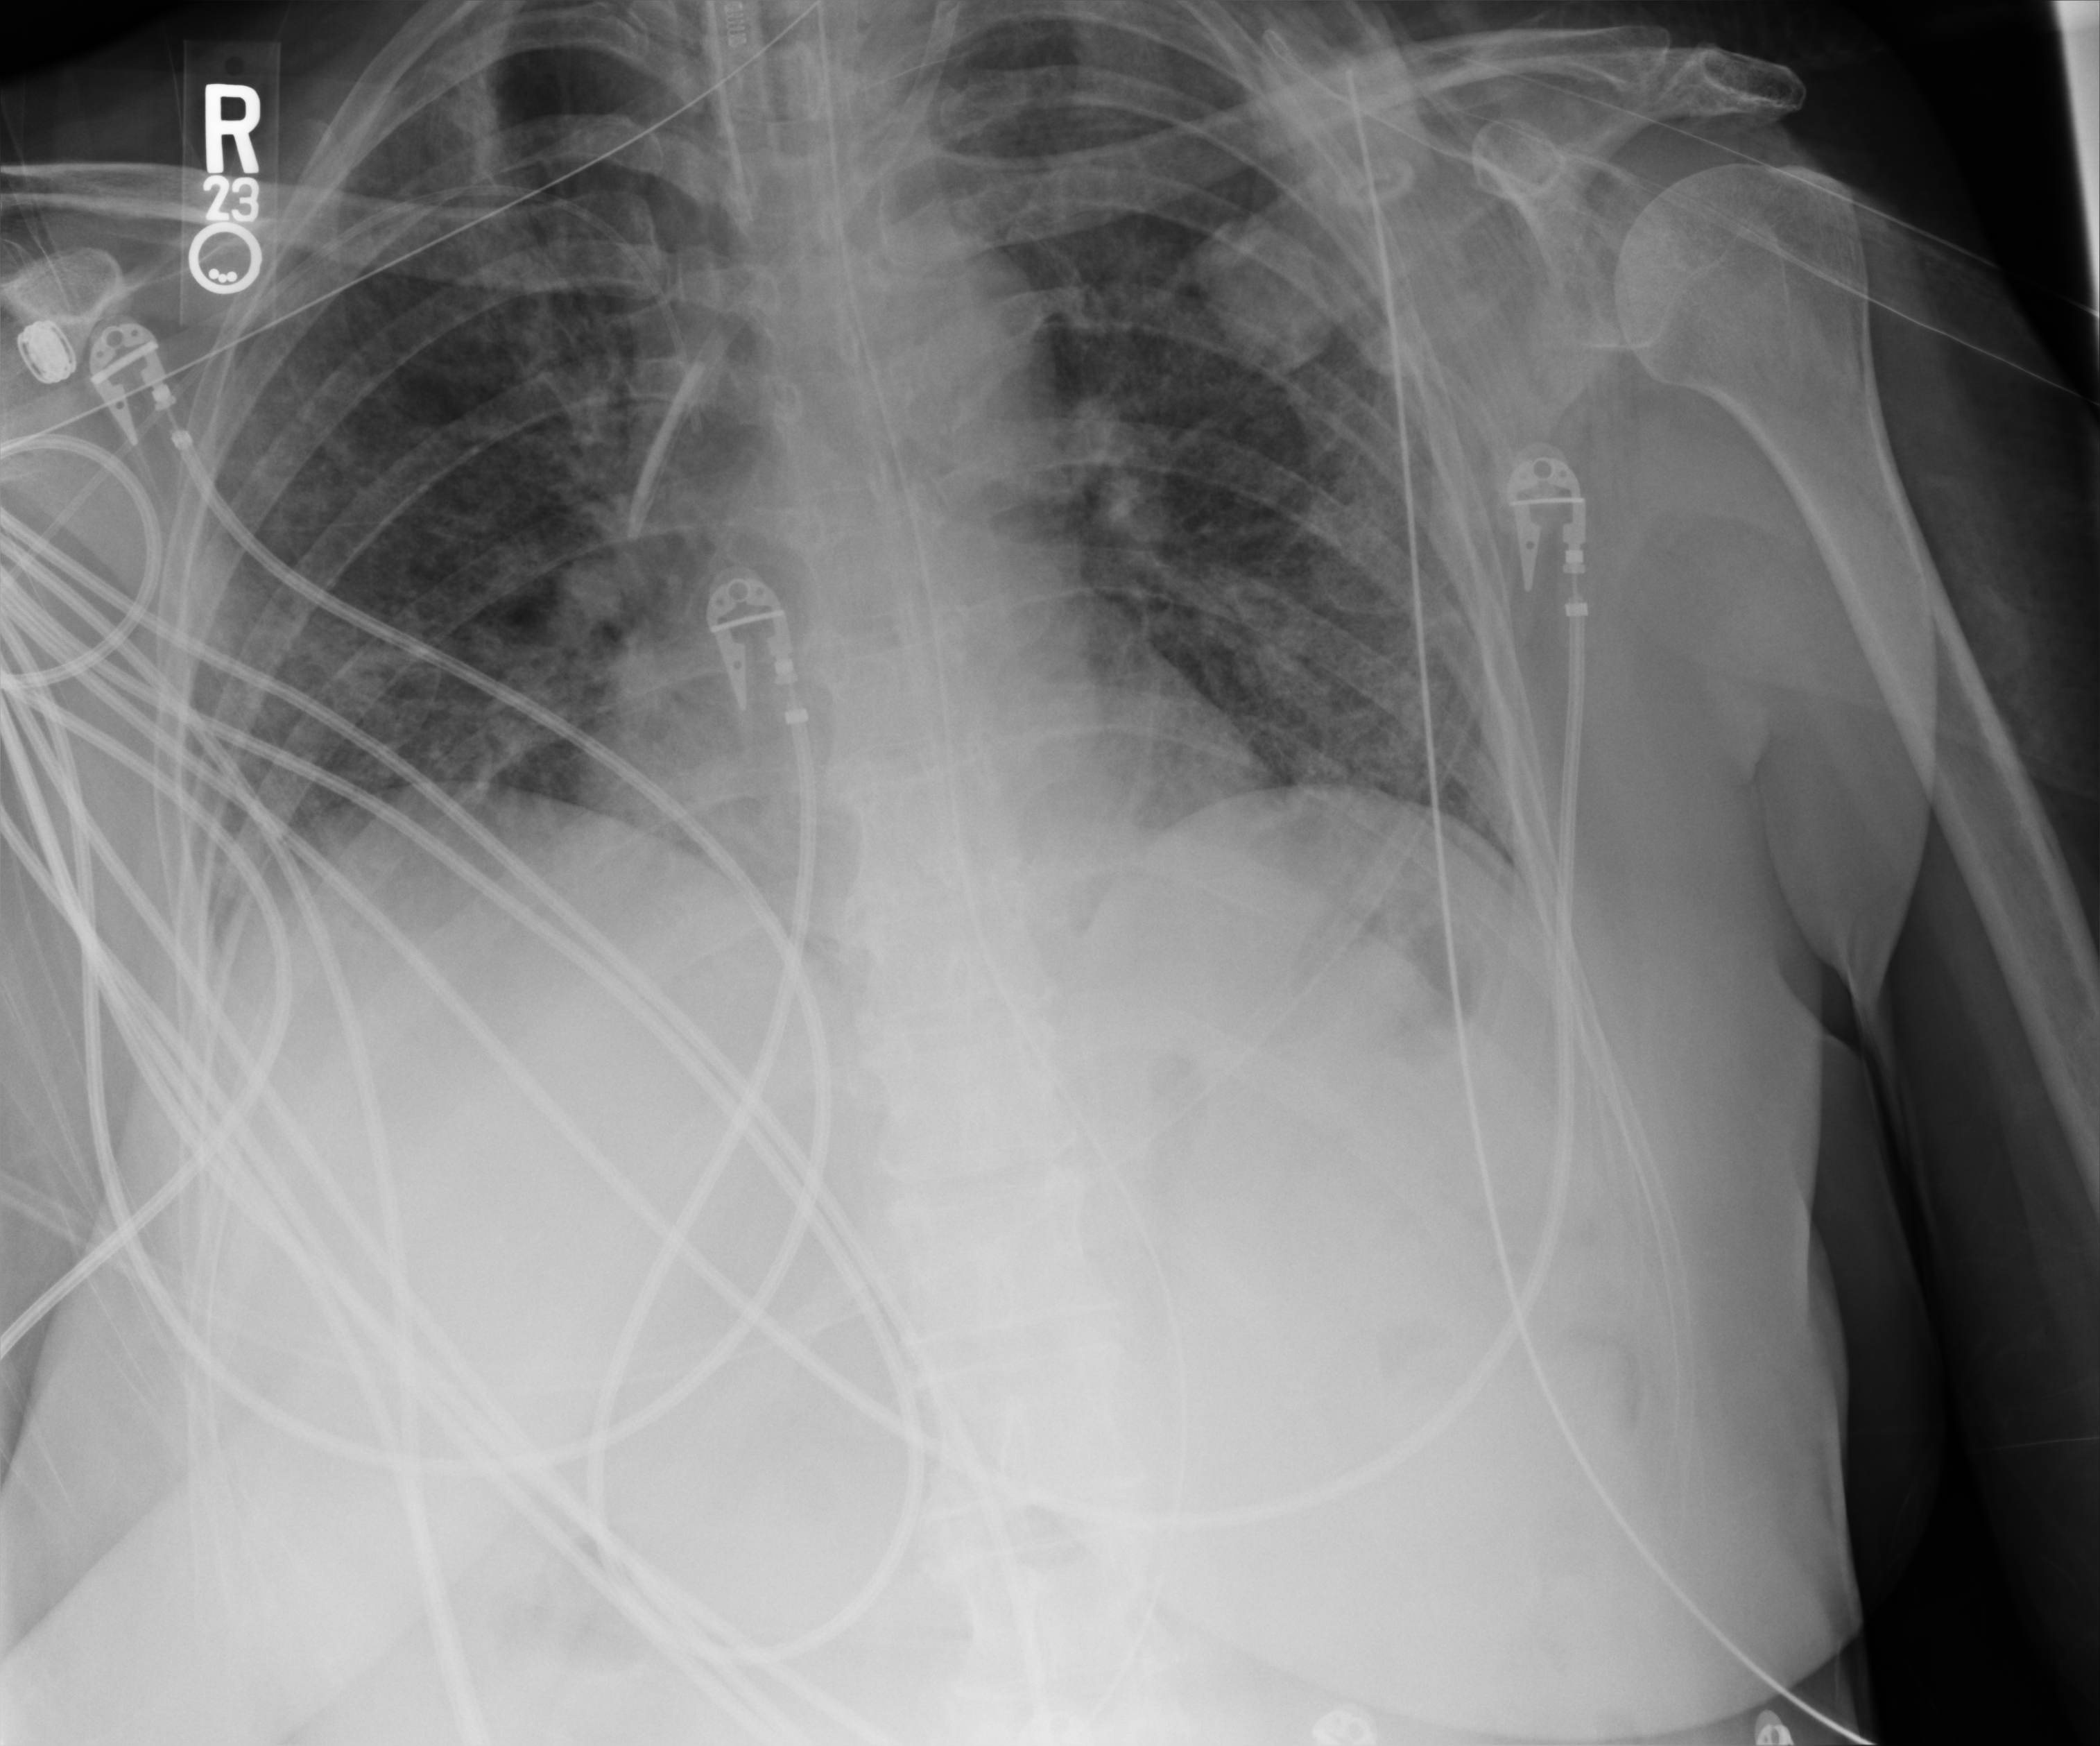
Chest X-ray (portable); anteroposterior (AP) projection. Female patient hospitalised with COVID-19, age 60–74 years.
Hospital-stay facts (about this admission, not read from this image; timing relative to this image not recorded):
- mechanically ventilated during this hospital stay: yes
- admitted to intensive care during this hospital stay: yes
- diabetes (admission record): no